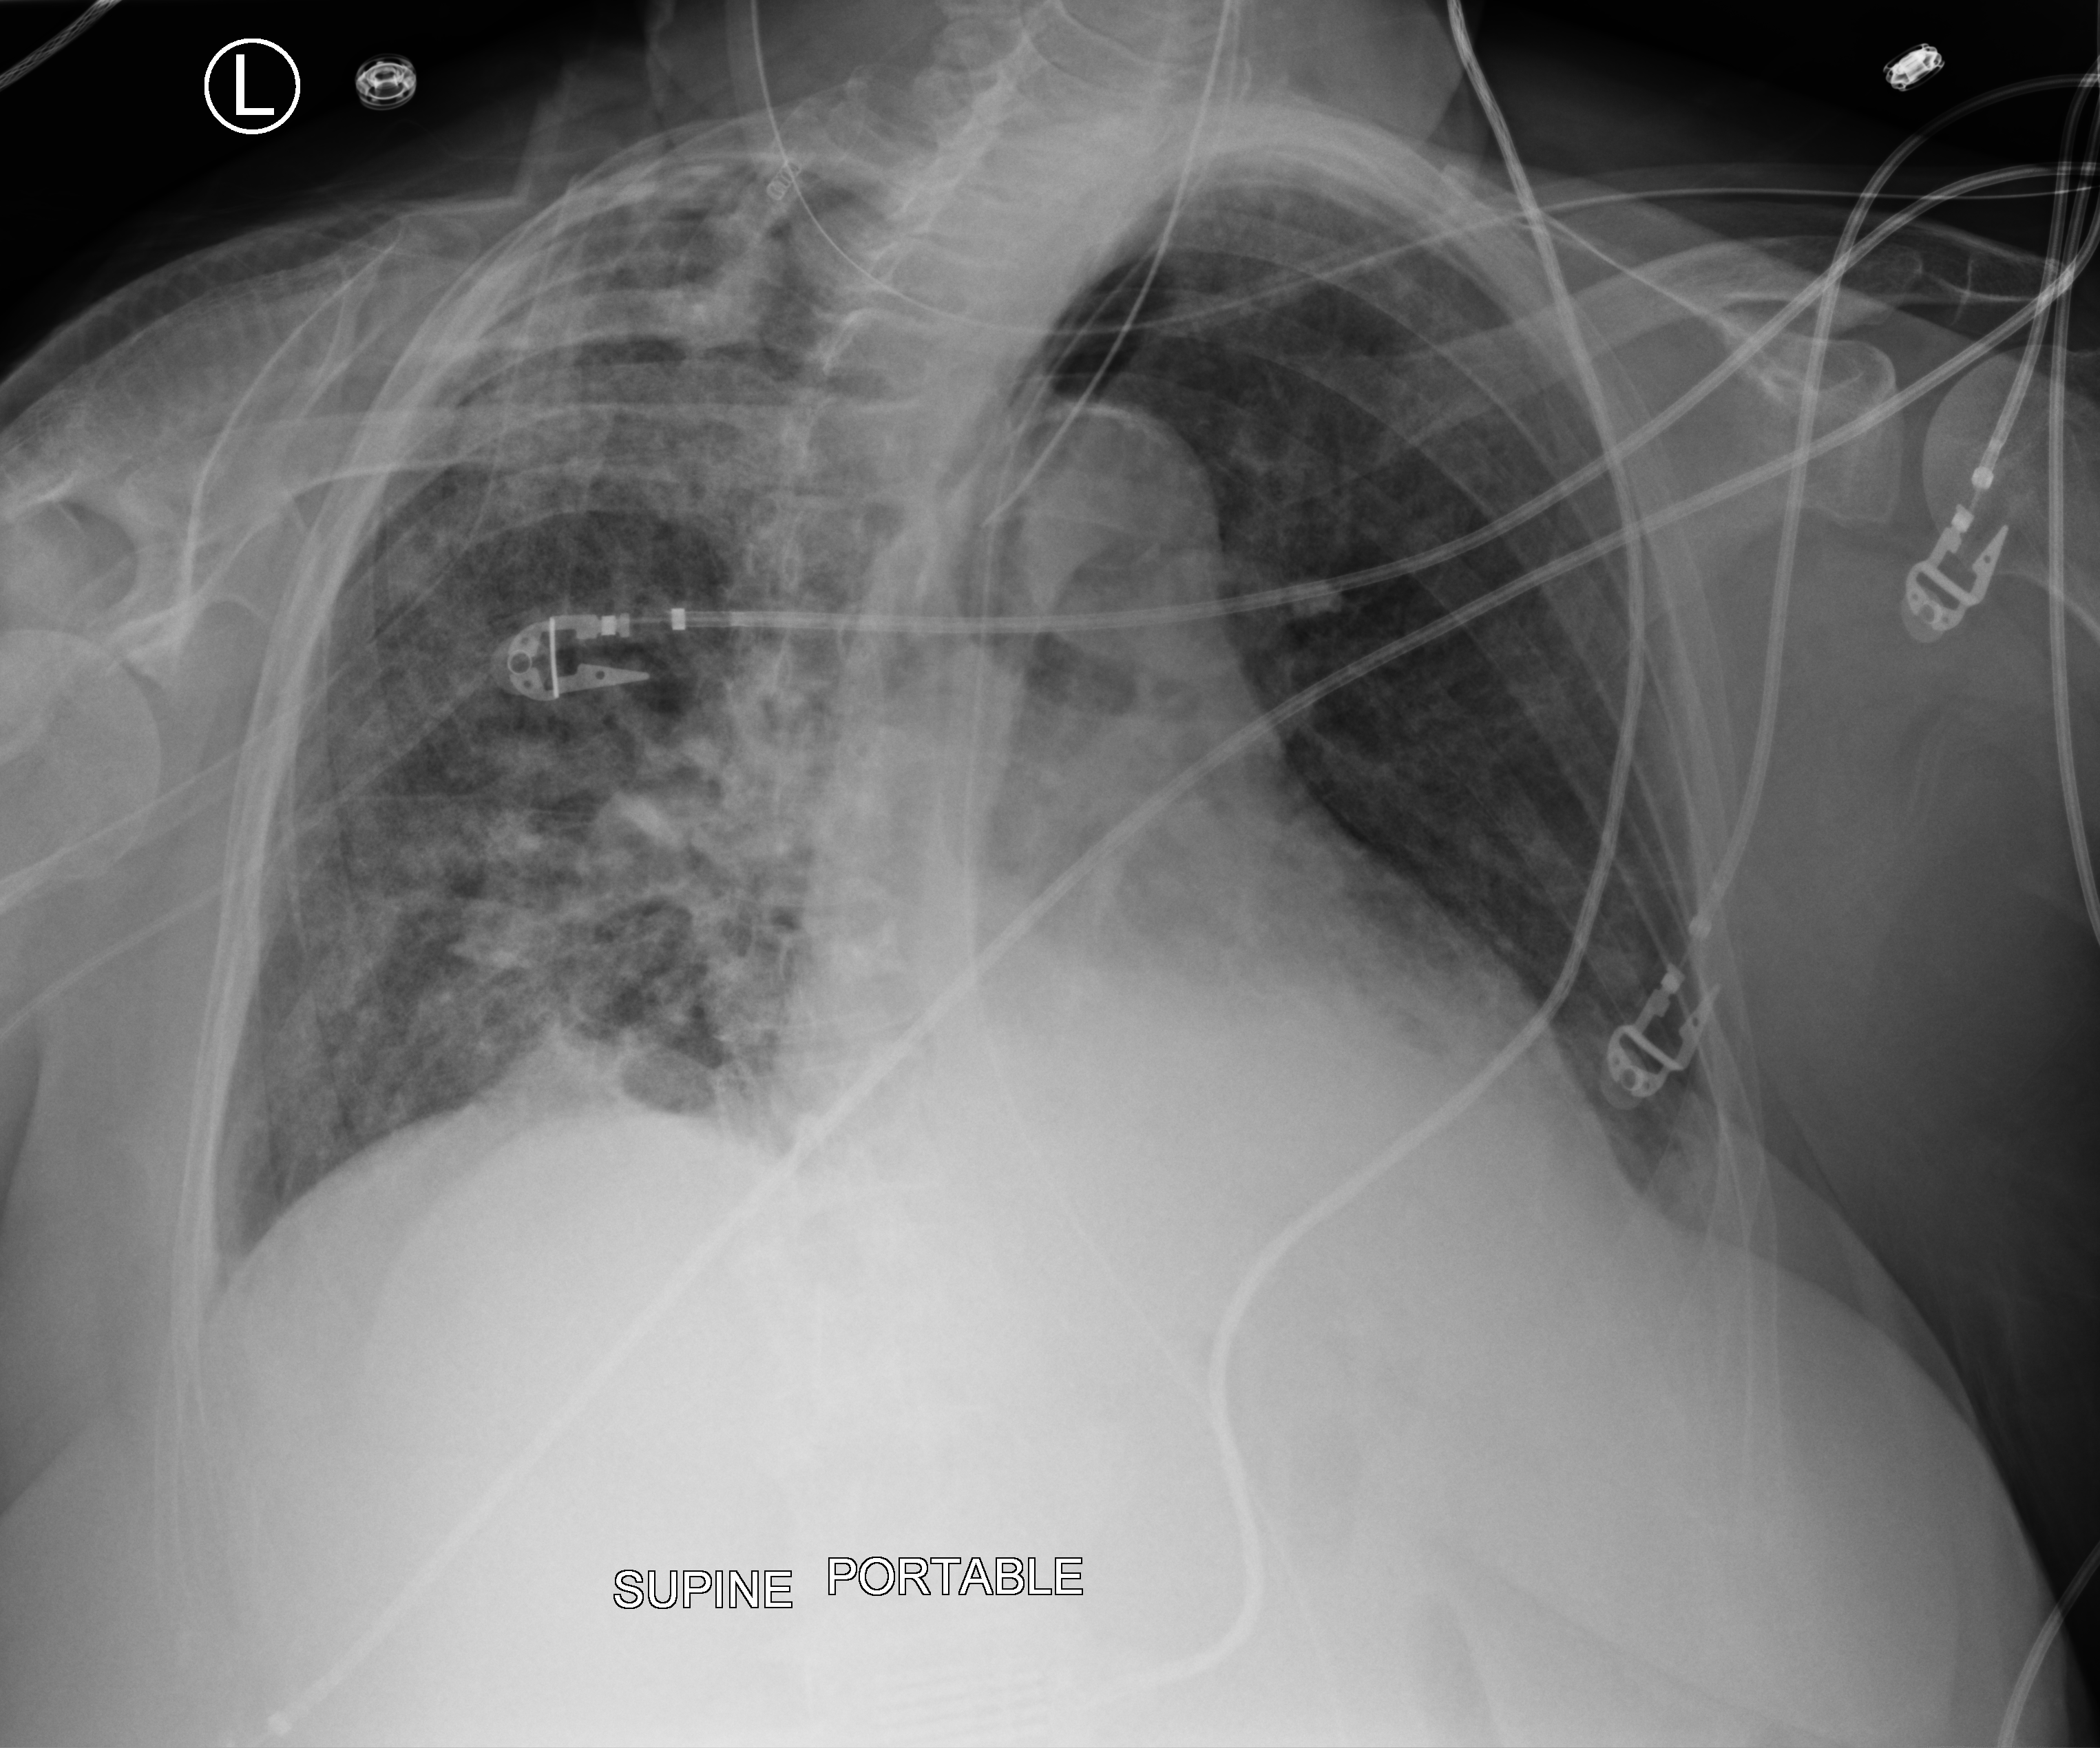
Portable chest radiograph; anteroposterior (AP) projection. Female patient hospitalised with COVID-19, age 75–90 years.
From the hospital-stay record, not from the radiograph (when in the stay this image was taken is not recorded):
- chronic kidney disease (admission record): no
- admitted to intensive care during this hospital stay: yes
- mechanically ventilated during this hospital stay: yes